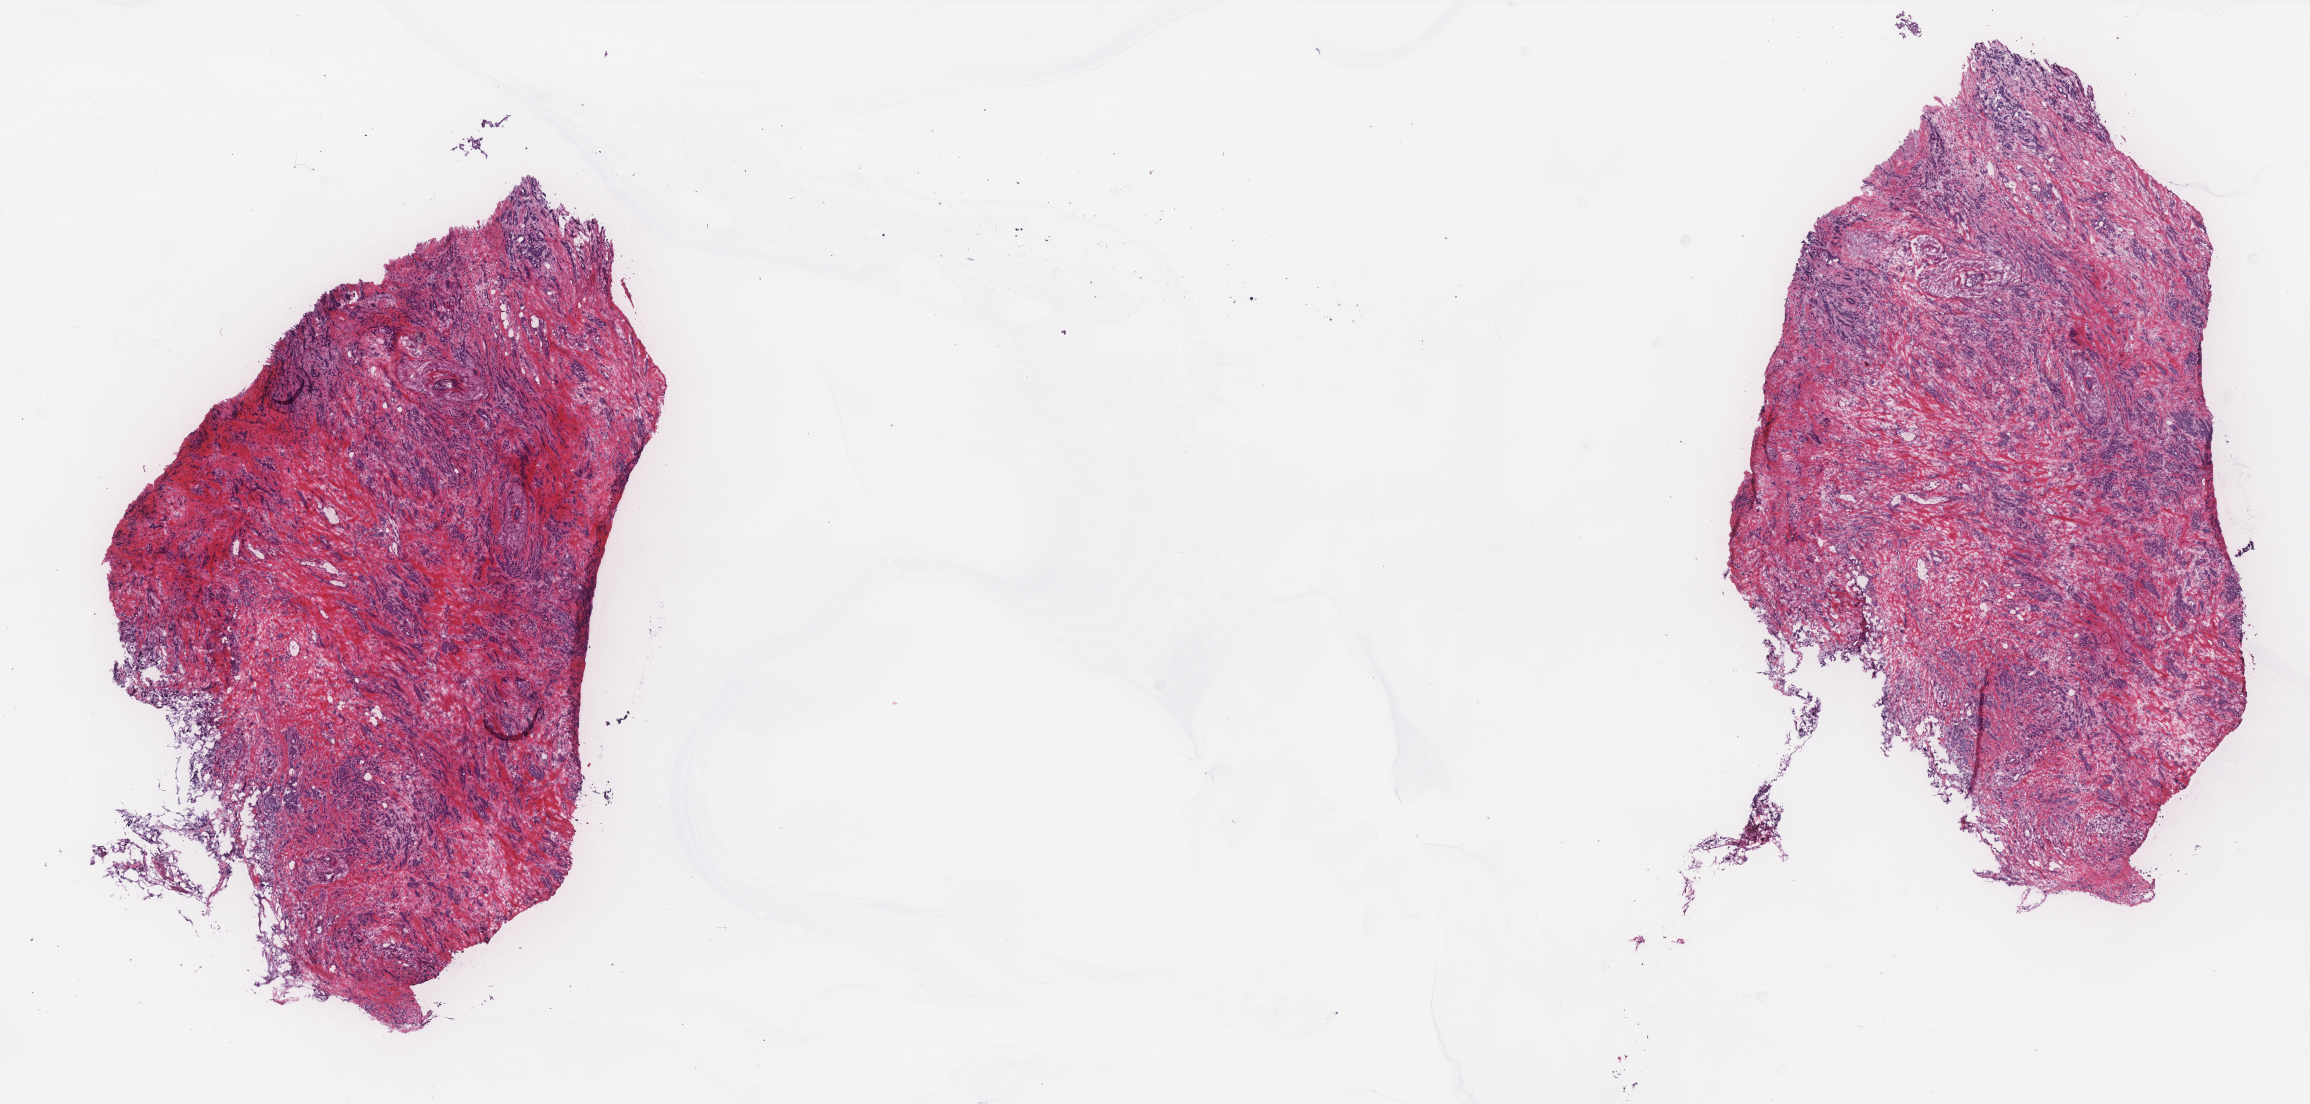
Whole-slide histology image, H&E — low-resolution overview of the scanned area, about 18.5 x 8.9 mm. Frozen section. Sample: primary tumour, breast. Female patient; age at initial diagnosis 84 years. Pathologist review of this section (percent, as recorded): tumour cells 55%, tumour nuclei 75%, normal cells 1%, stromal cells 43%, necrosis 1%. Infiltration values recorded for this section: lymphocyte infiltration 1%, monocyte infiltration 0%, neutrophil infiltration 0%.
Lymph nodes positive (case pathology): 0 of 1 examined. Pathologic diagnosis: Lobular carcinoma, NOS. AJCC pathologic stage: IIB. Laterality: right.